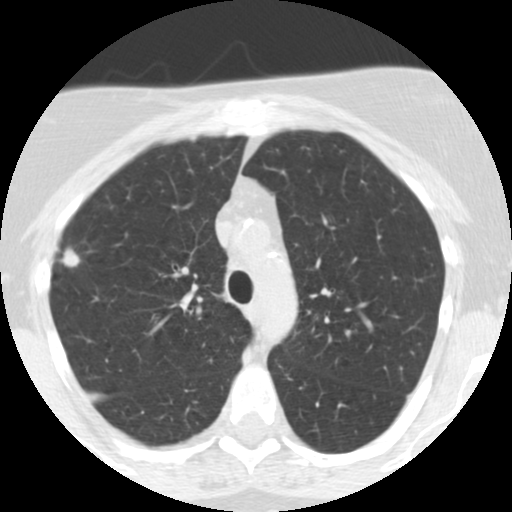
Low-dose screening chest CT, one axial slice. Position 181 of 248 along the scan axis. Reconstruction kernel STANDARD. 120 kVp. Lung window (W 1500 / L -600 HU). 2.5 mm slice thickness. 512 × 512 image matrix, field of view 287 × 287 mm.
Annotated regions visible in this slice (manually delineated by an expert):
- lesion 1 (tumor, upper lobe of right lung): bounding box <60,248,80,267> (left, top, right, bottom; pixels)